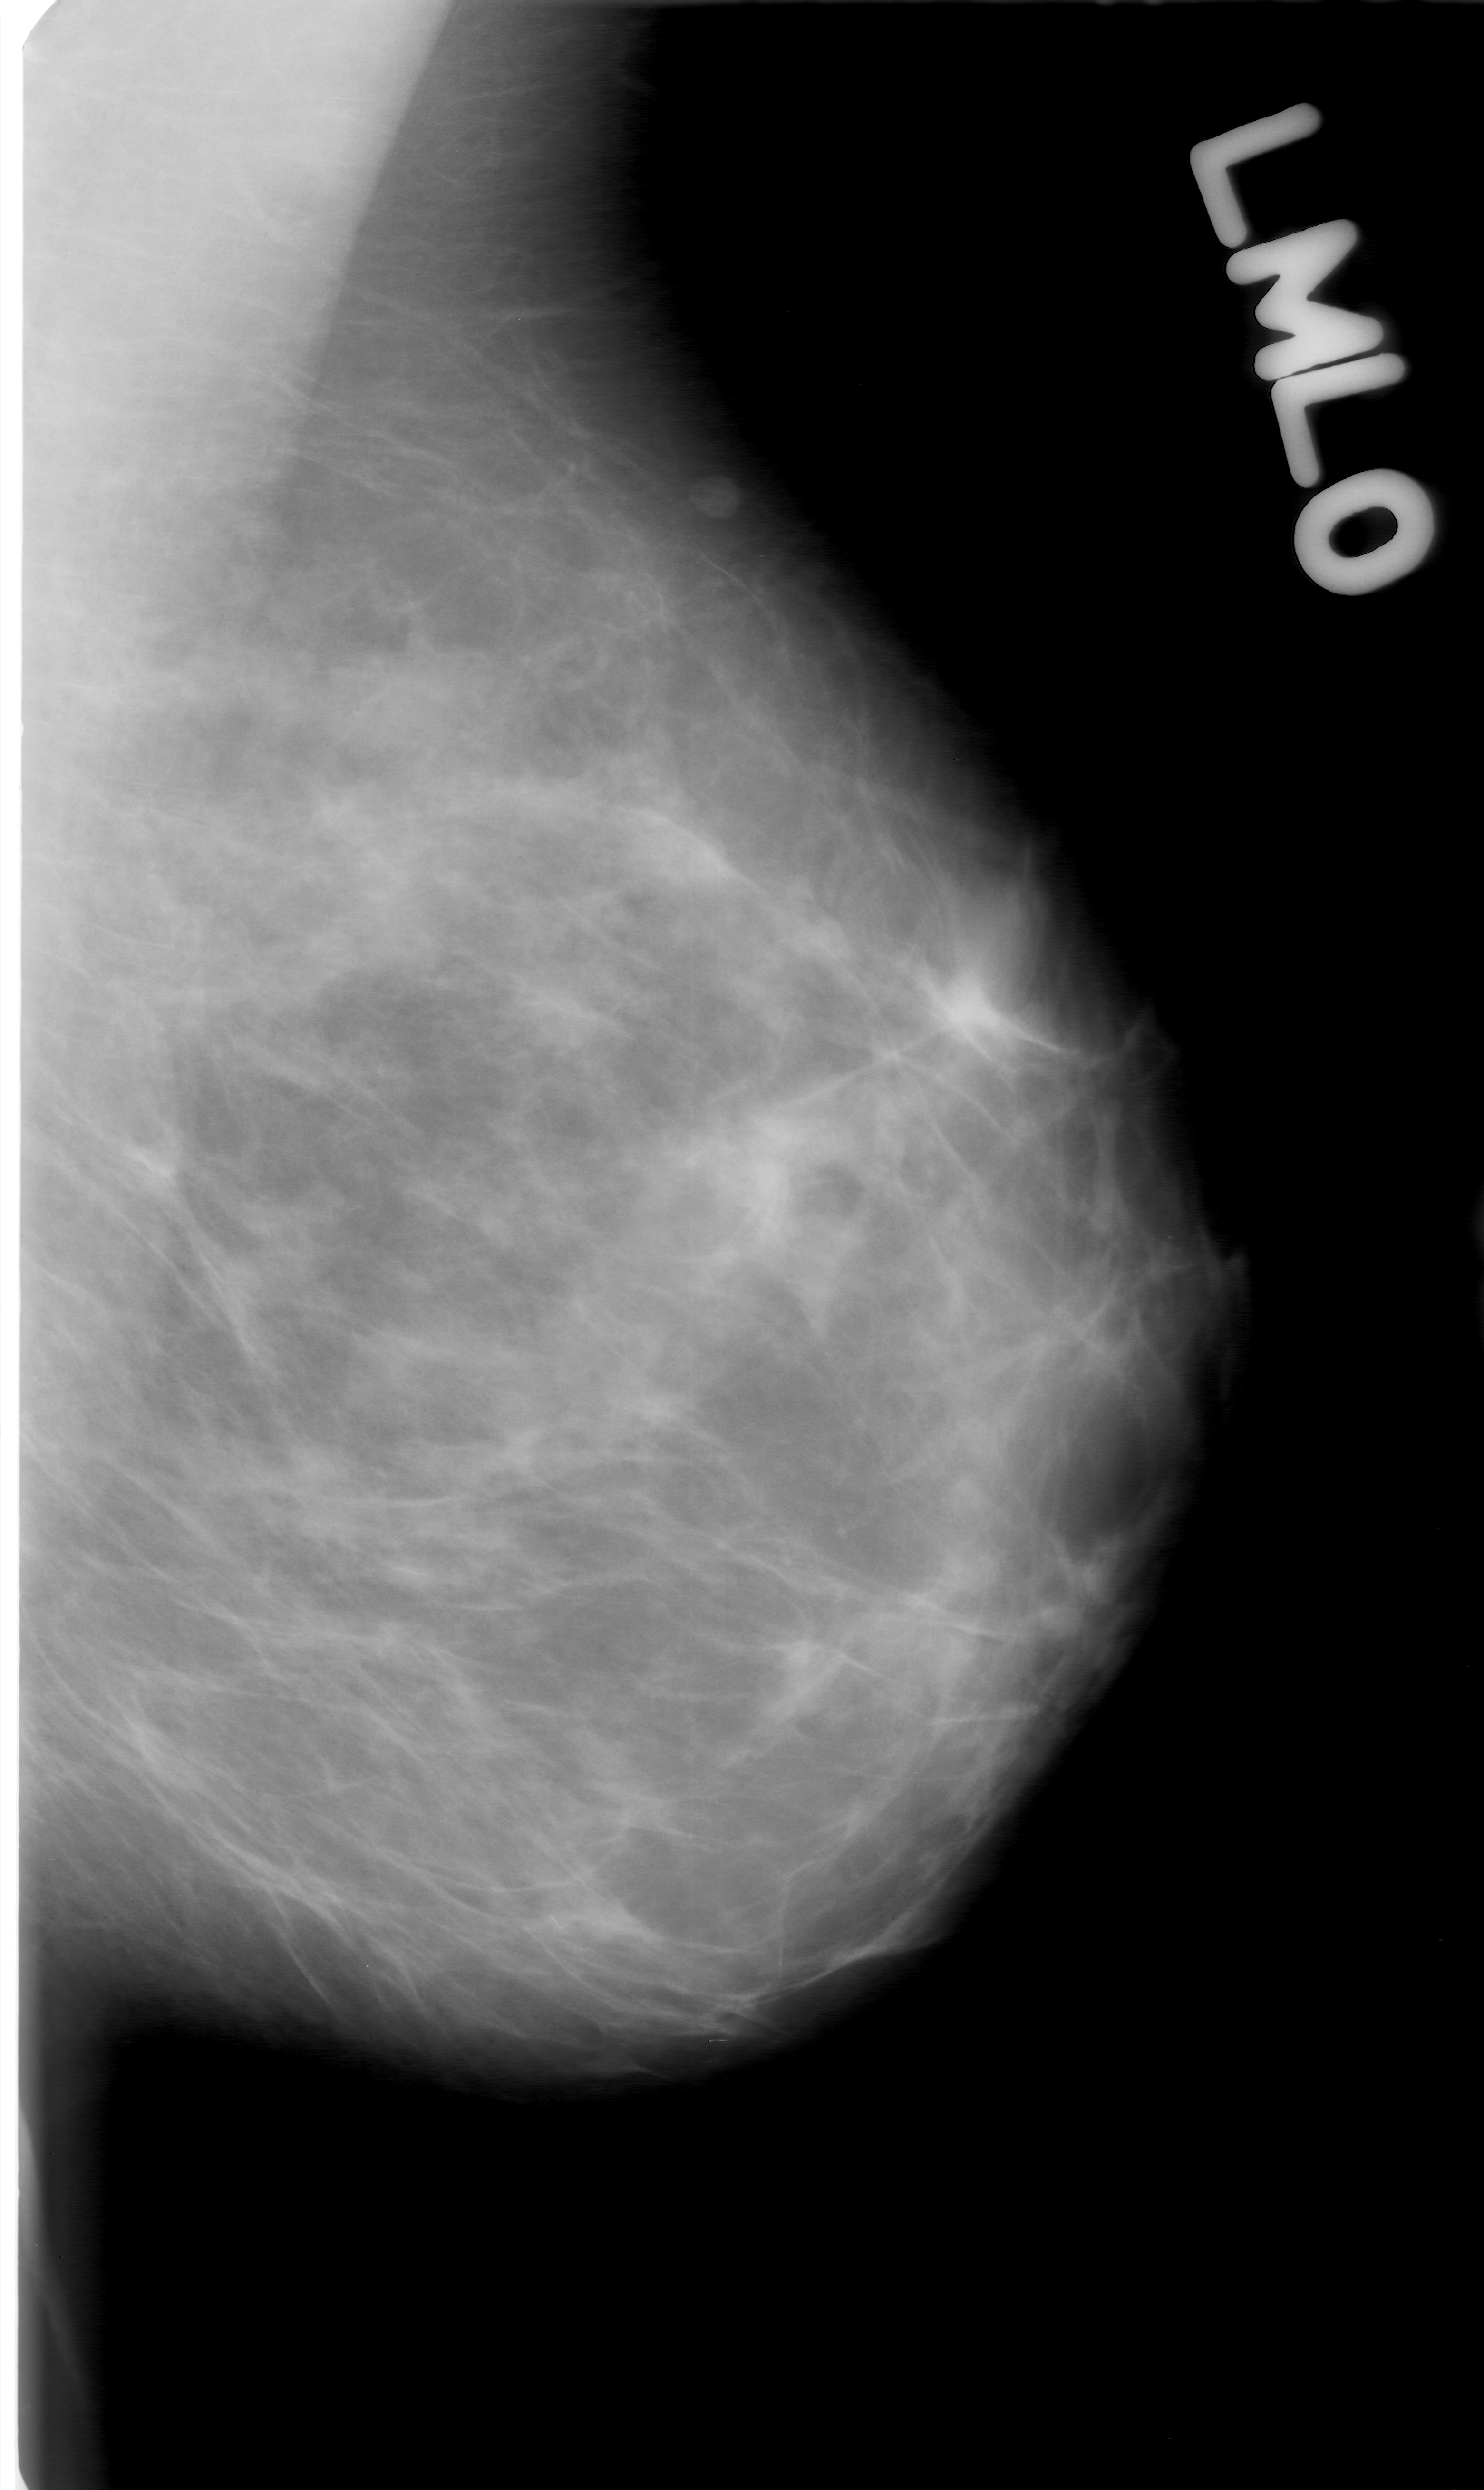
Mammogram (digitized film); left breast; mediolateral oblique (MLO) view; BI-RADS breast density category 2 (scale 1–4).
- Radiologist-marked abnormalities on this image: mass, shape oval, margins obscured; BI-RADS assessment category 0 (incomplete: needs additional imaging); subtlety rating 5 on a 1 (subtle) to 5 (obvious) scale; pathology (as recorded): benign.